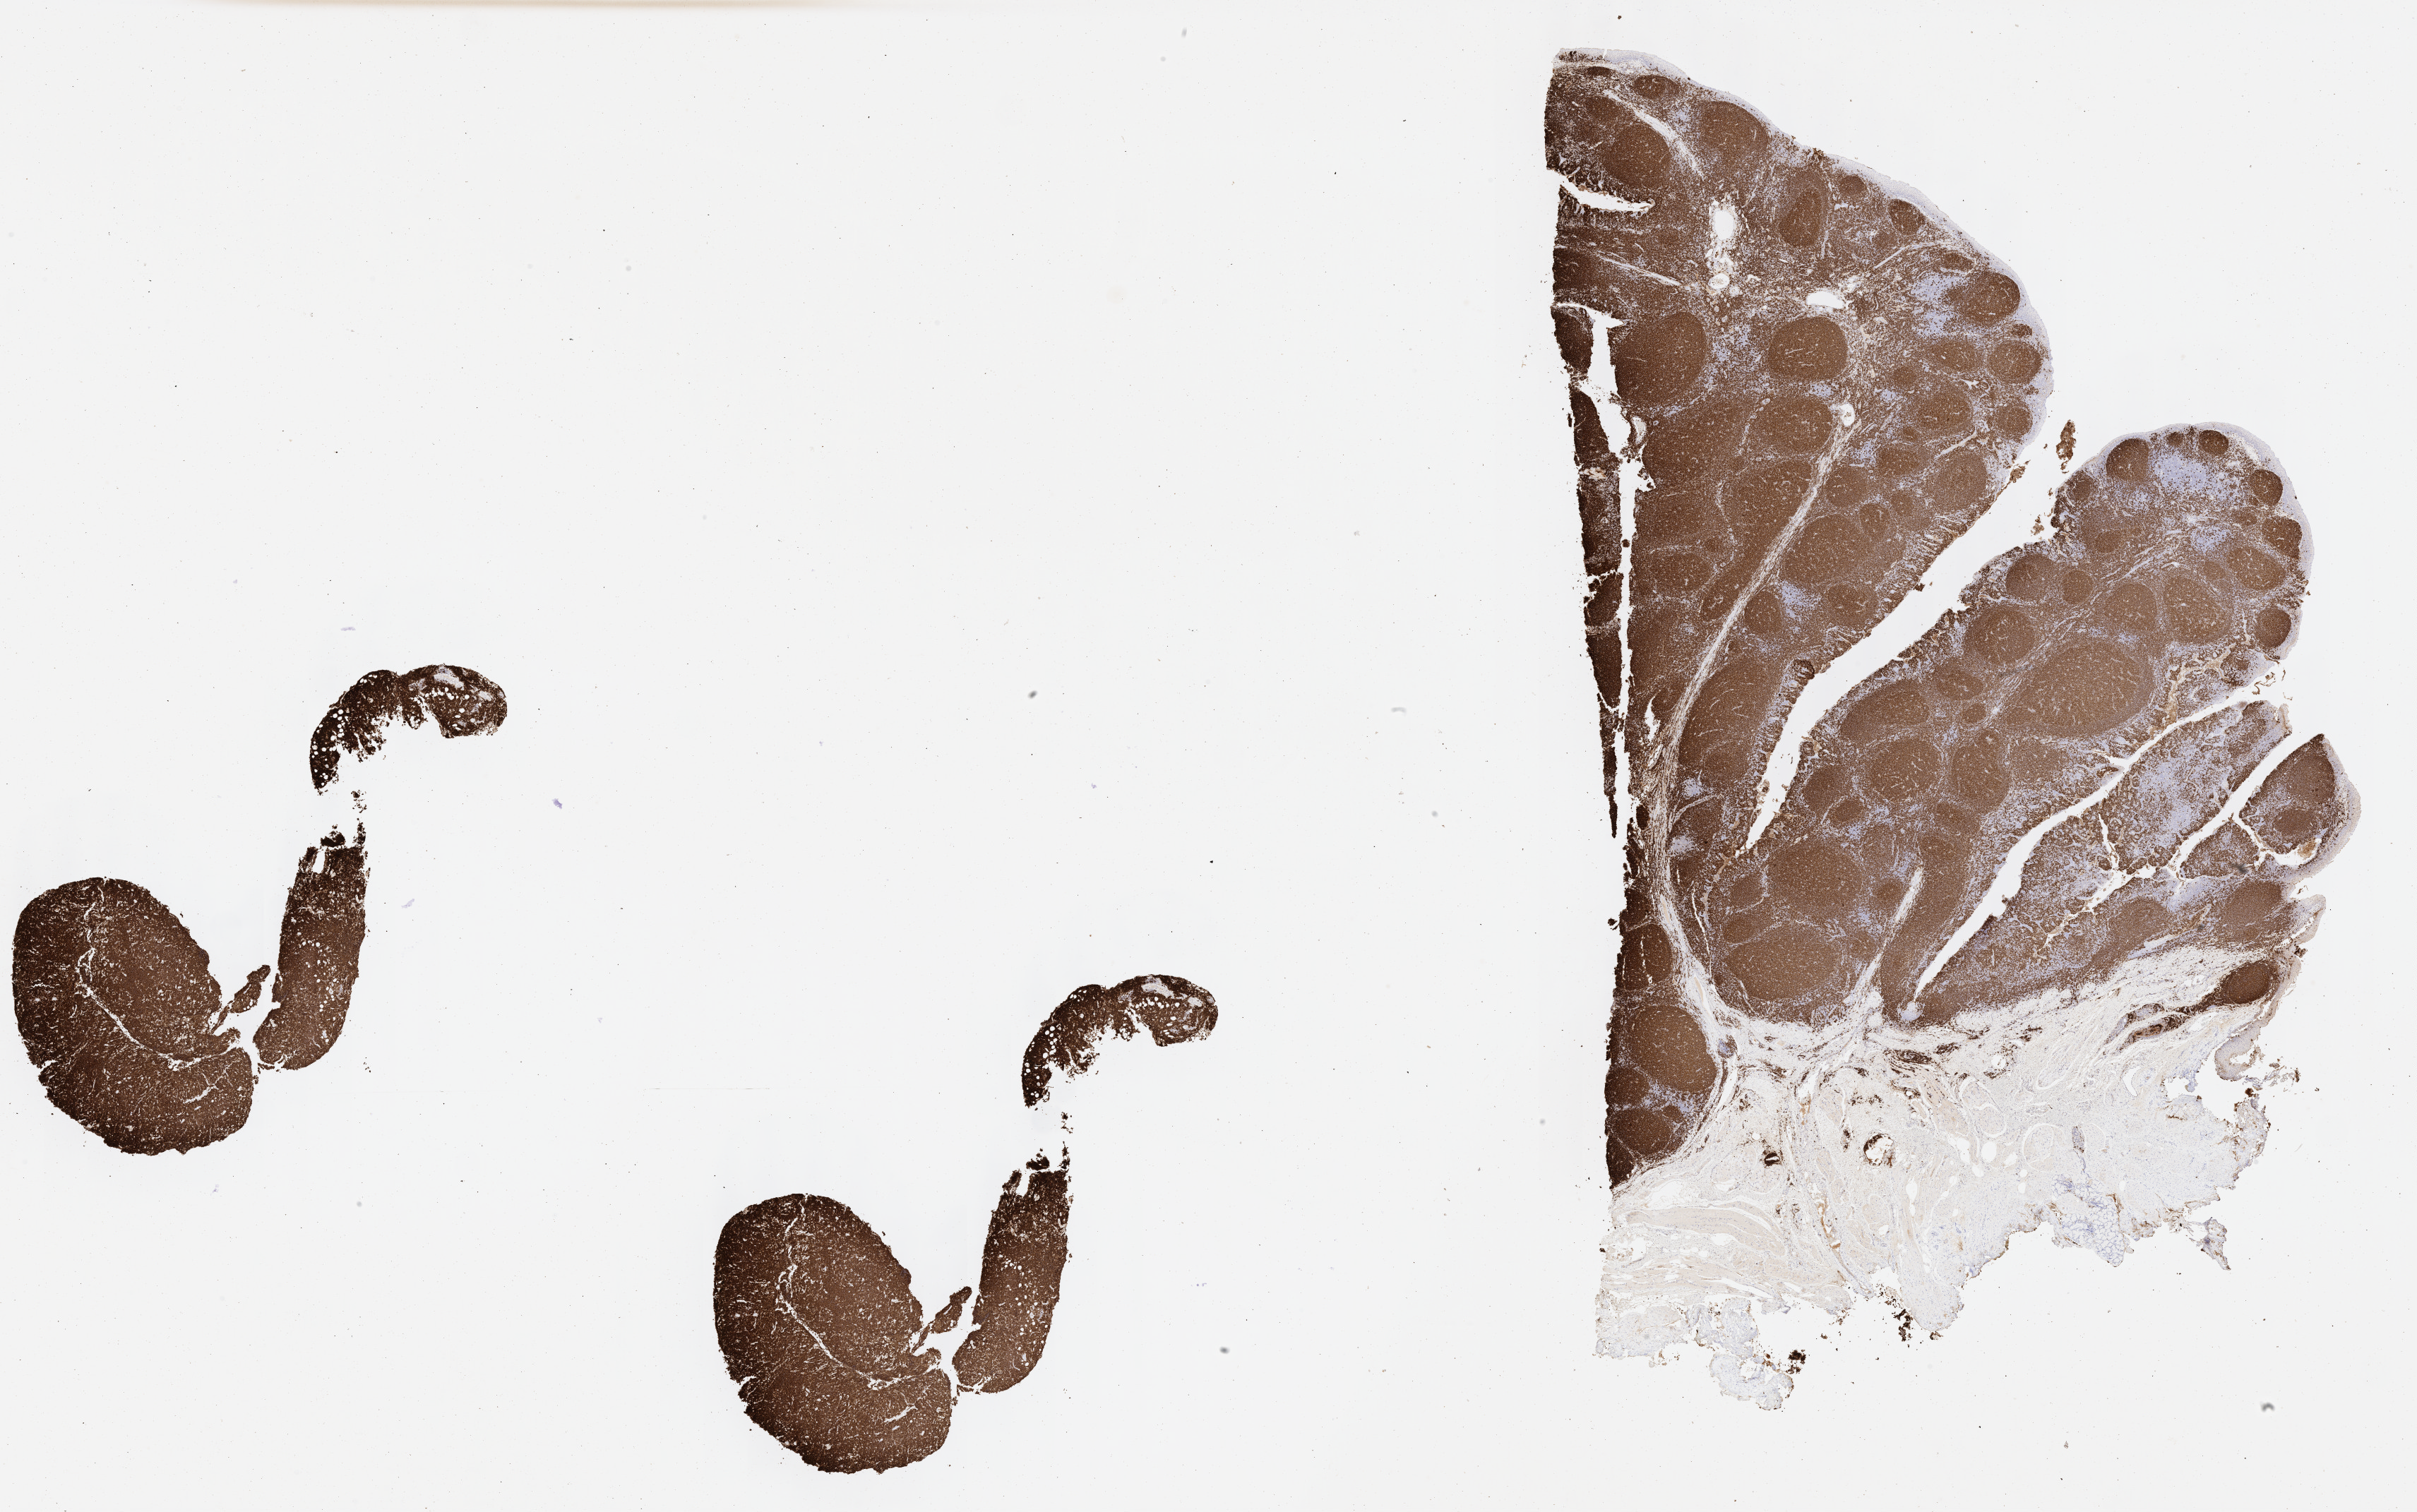
Immunohistochemistry (IHC) whole-slide image stained for CD20, low-resolution overview of the scanned area, about 27.7 x 17.3 mm. Tumor tissue. Site: head and neck. Patient female; 55 years old.
* histologic diagnosis: Burkitt lymphoma, NOS